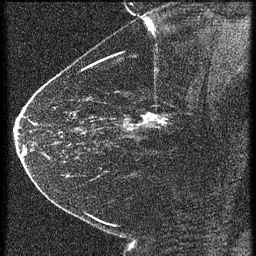
Breast MRI (dynamic contrast-enhanced), one sagittal slice; slice 41 of 60 in the series (ordered by position); 4 images stored at this slice position (order not interpretable as contrast timing); 1.5 T; TE 4.2 ms, TR 21.3 ms; 1.5 mm slice thickness; 256 × 256 image matrix, field of view 180 × 180 mm. Female patient, age 43 years. Case-level facts recorded for this patient, not image findings: setting: breast cancer imaged before/during neoadjuvant chemotherapy; receptor status: HER2-positive.
Structures marked on this image (semi-automatically segmented with operator editing):
- analysis volume of interest (the breast-tissue region the enhancement analysis was run in; not a lesion): bounding box <122,100,187,151> (left, top, right, bottom; pixels)
- tumour enhancement mask (voxels above the 90 % enhancement threshold inside the analysis volume of interest): <132,114,167,127>